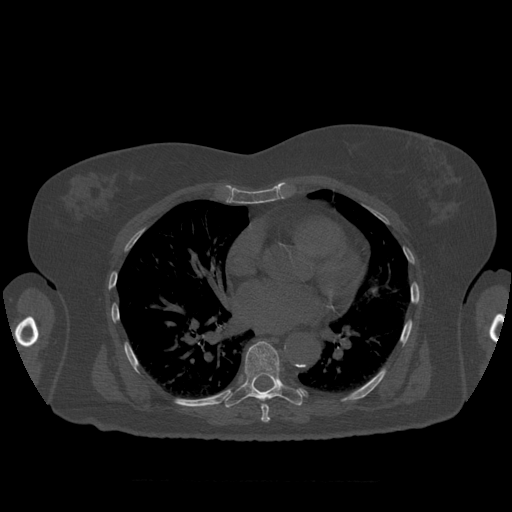
CT including the spine, one axial slice; position 382 of 399 along the scan axis; bone window (W 1800 / L 400 HU); 1.25 mm slice thickness; 512 × 512 image matrix. Patient age 81 years. Case-level facts recorded for this patient, not image findings: primary cancer: renal.
Outlined on this slice (semi-automatic segmentation, software-assisted and operator-edited):
- T7 vertebra: bounding box (x1, y1, x2, y2) in pixels: (261, 404, 270, 423)
- T8 vertebra: (224, 341, 303, 408)